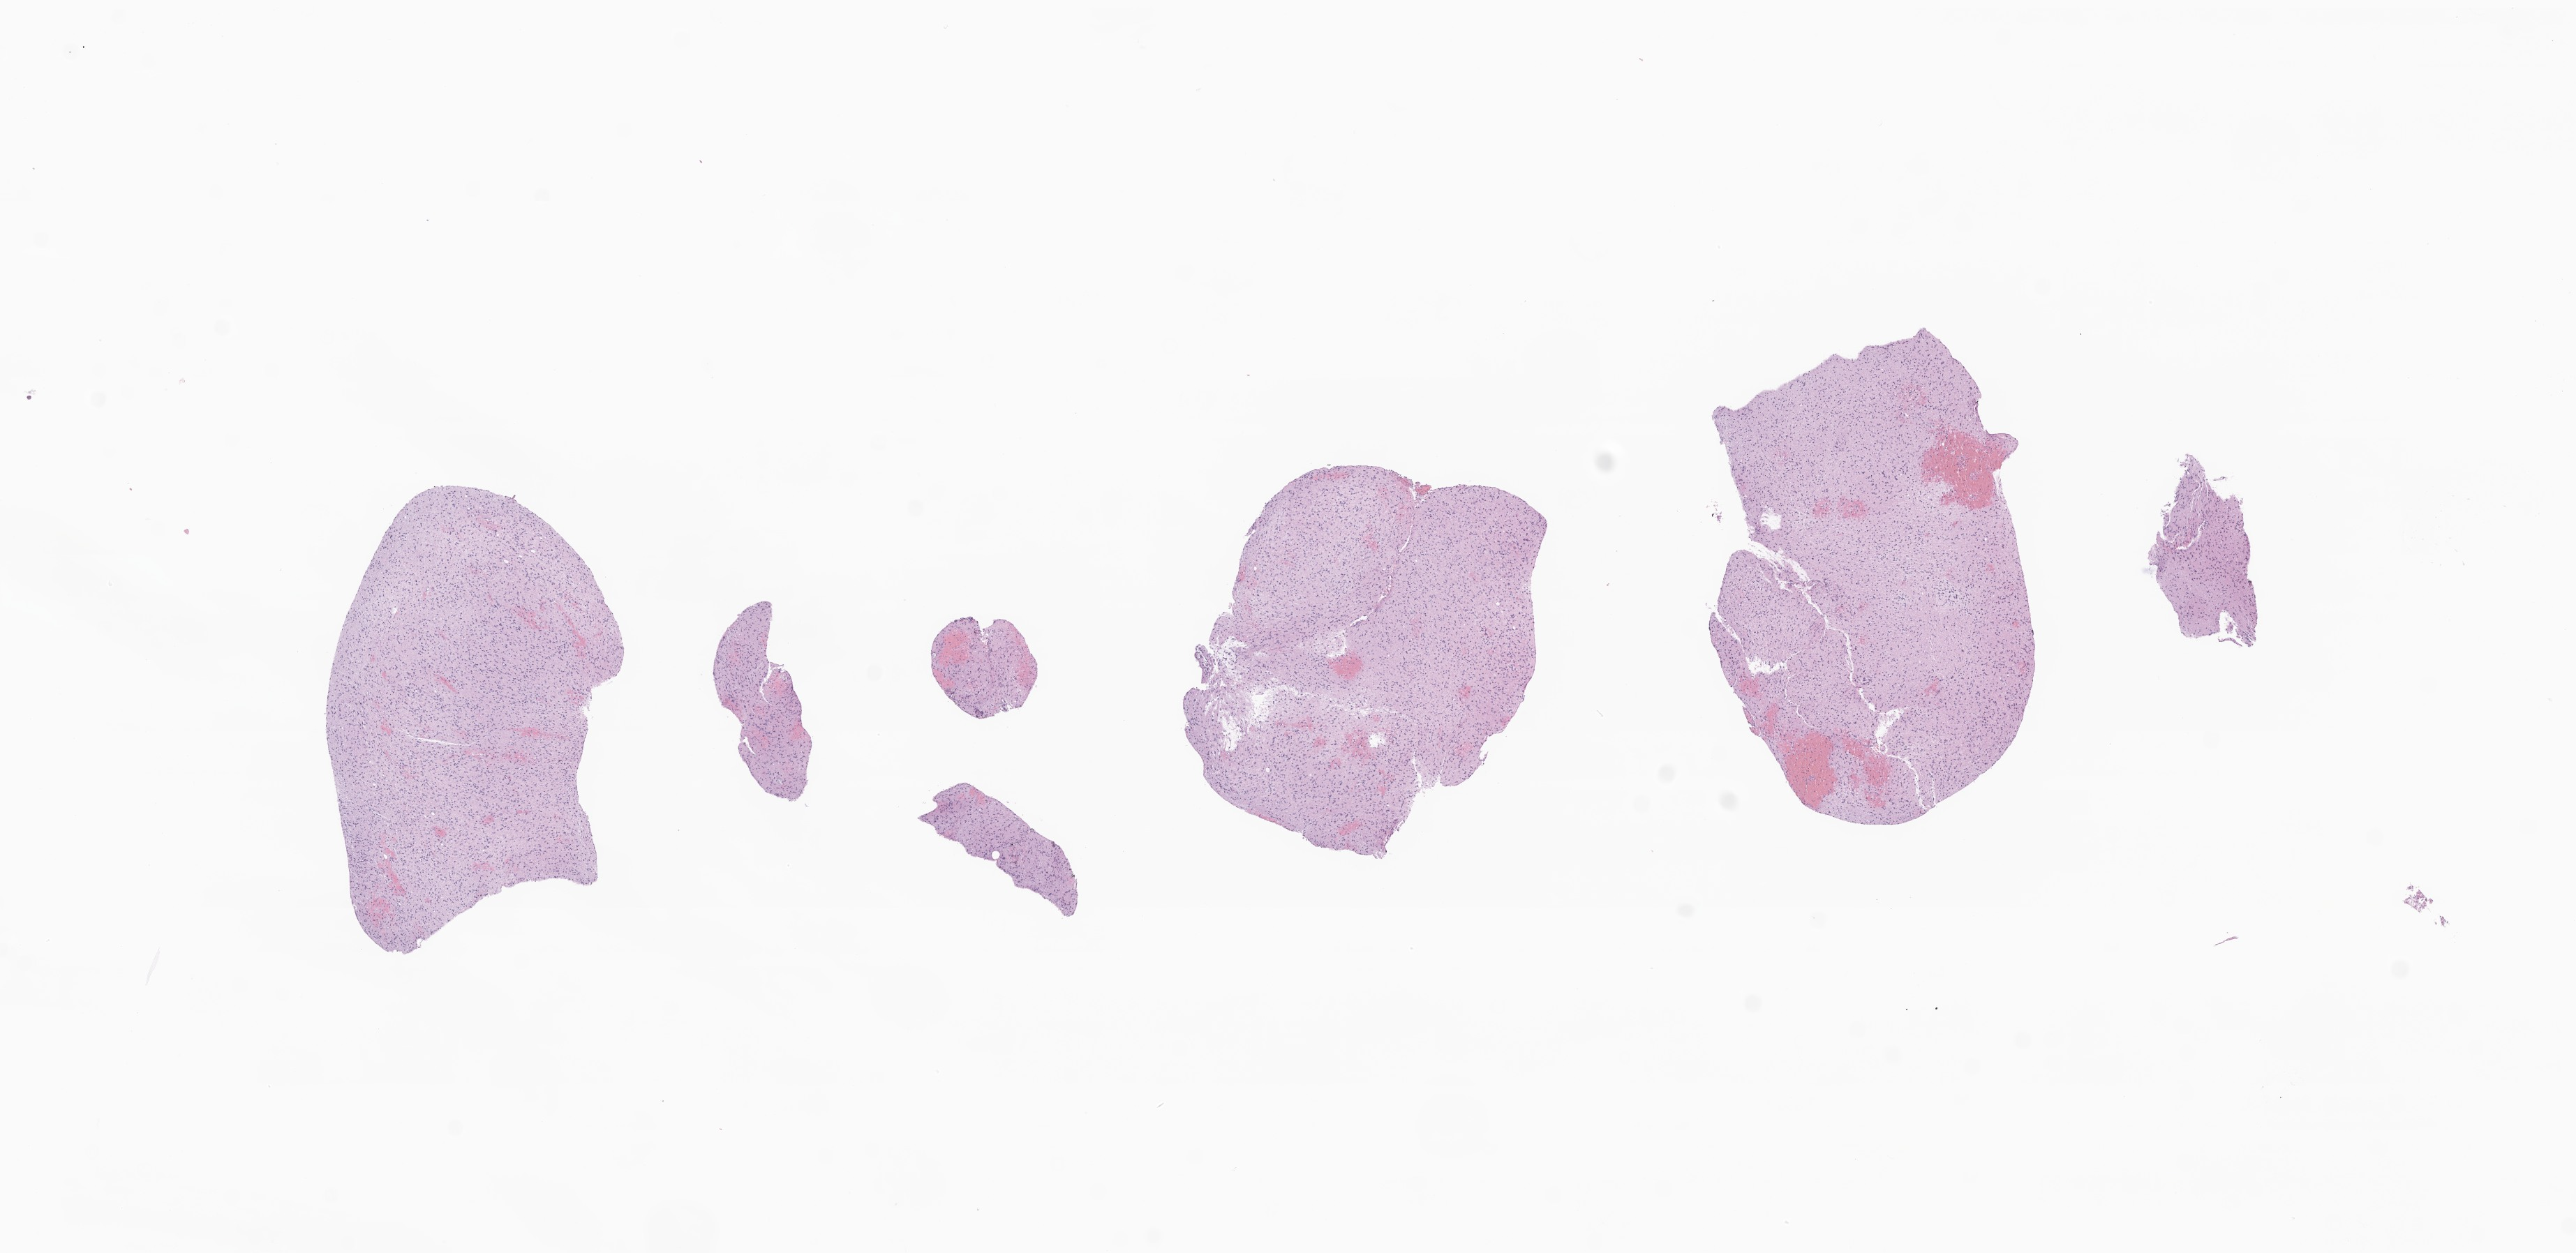
H&E whole-slide image of tumor tissue from the brain, a low-resolution overview of the entire scanned area, about 15.6 x 7.6 mm; formalin-fixed paraffin-embedded section. Patient male; age 314 months (26 years 2 months).
Recorded diagnosis: Astrocytoma, NOS.